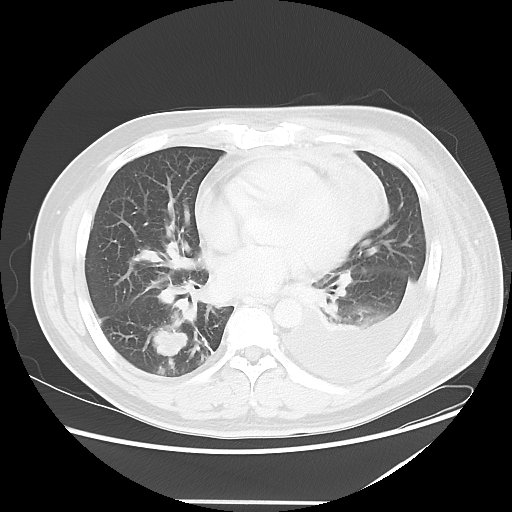
Chest CT, one axial slice; slice 22 of 52 in the series (ordered by position); 120 kVp; lung window (W 1500 / L -600 HU); 5 mm slice thickness; 512 × 512 image matrix. Patient: male, 42 years. From the clinical record (not read from this slice): clinical TNM (as recorded): T2 N1 M1.
Annotated regions visible in this slice (bounding box drawn by a radiologist):
- lung tumour (recorded histology: adenocarcinoma): box from (x=149, y=325) to (x=199, y=366) px